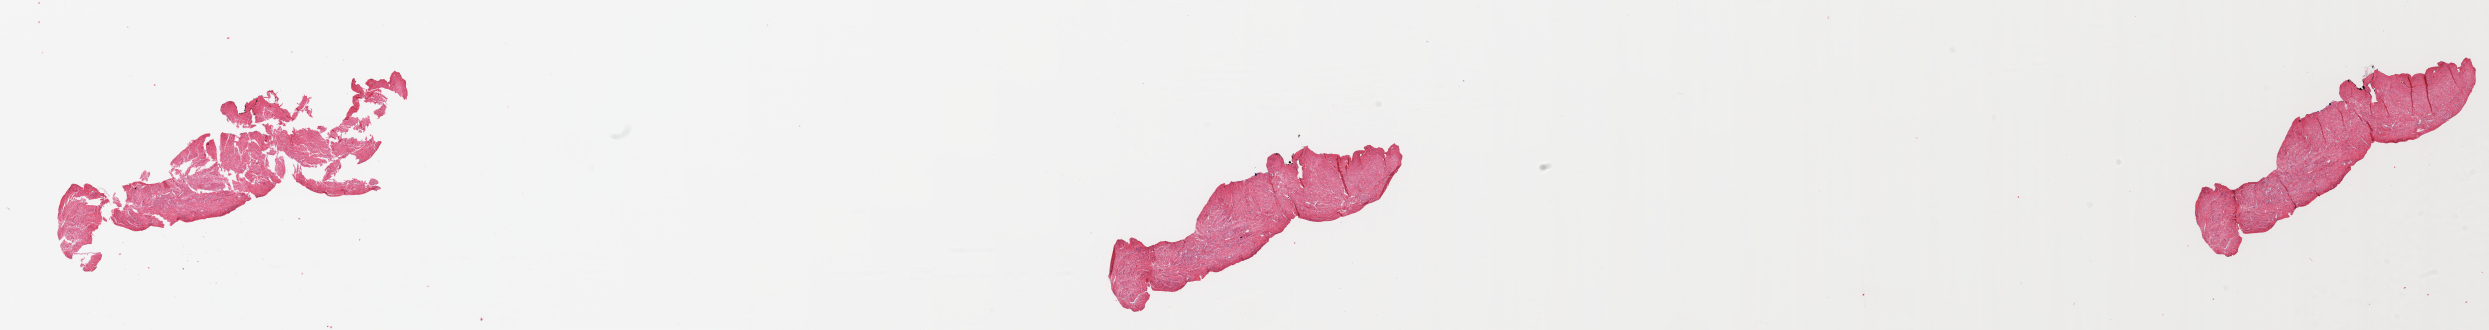
Whole-slide histology image, H&E — whole scanned area (about 39.4 x 5.2 mm, slide scanned at 20x) shown as a low-resolution overview; uterus, normal (non-tumour) tissue. 72-year-old female patient.
This section: normal (non-tumour) tissue from the same patient. Patient diagnosis: Endometrioid adenocarcinoma, NOS.